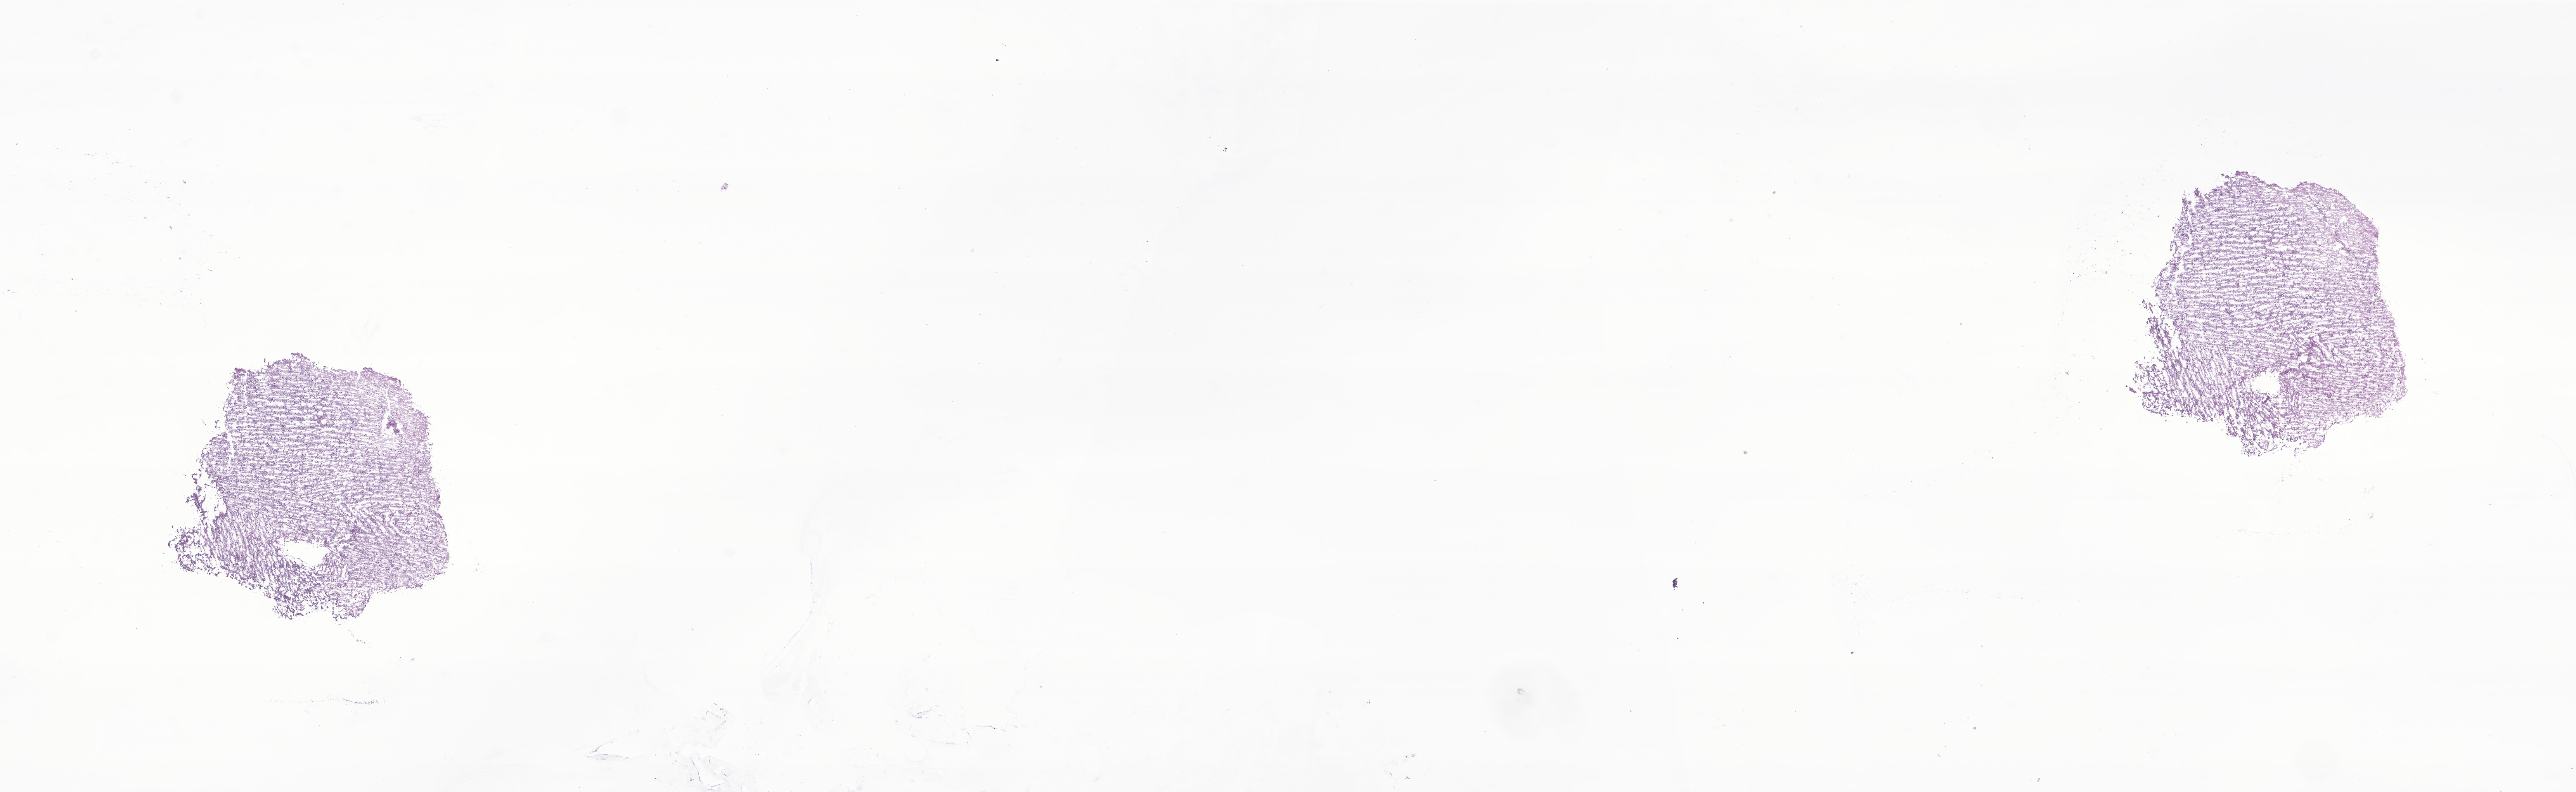
Haematoxylin and eosin whole-slide image of tumor tissue from the cerebrum, low-resolution overview of the scanned area, about 28.0 x 8.6 mm. Frozen section (OCT-embedded). Male patient, age 187 months (15 years 7 months).
- diagnosis (ICD-O-3 morphology term): Glioma, malignant